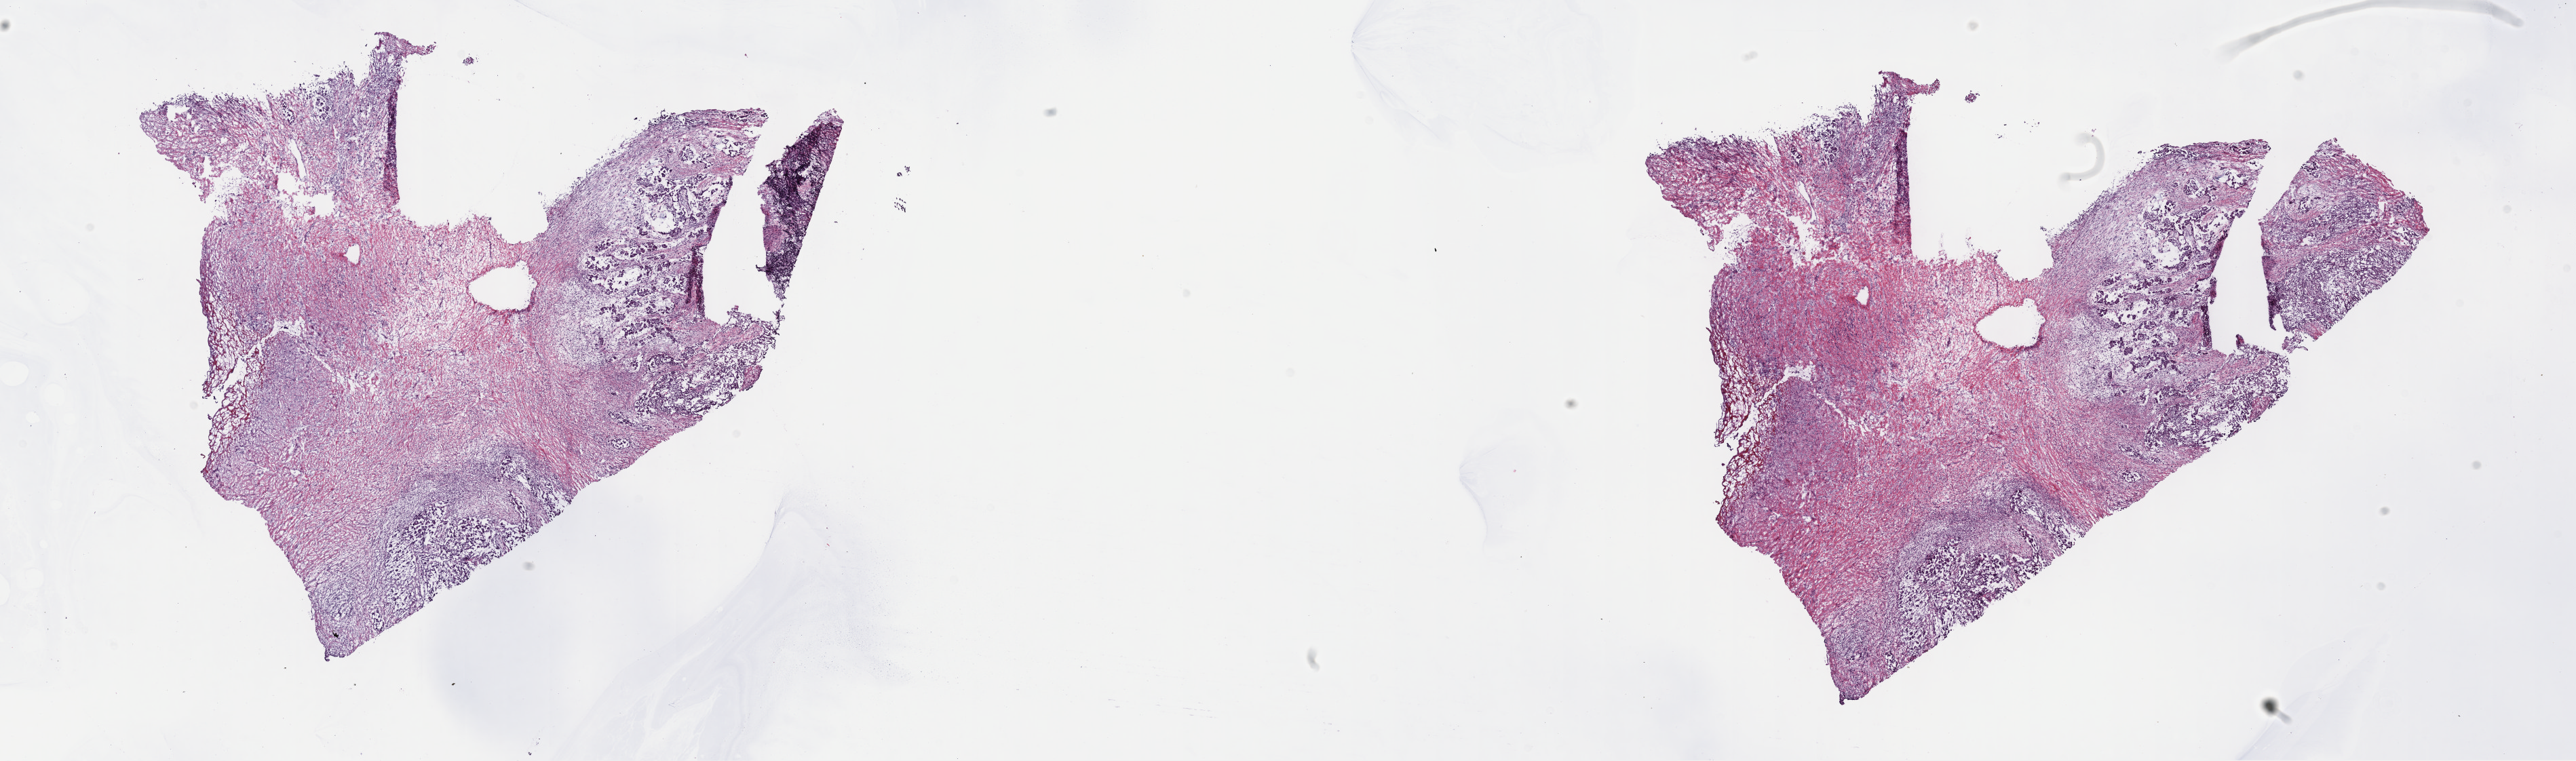
Whole-slide histology image, H&E-stained, shown as a low-resolution overview of the whole scanned area (about 30.7 x 9.1 mm, acquisition: 40x scan). Frozen section from the top of the tissue portion. Mesothelium, primary tumour sample. Male, age 68 years at initial diagnosis.
Histologic diagnosis: Mesothelioma, biphasic, malignant (pleura, NOS).